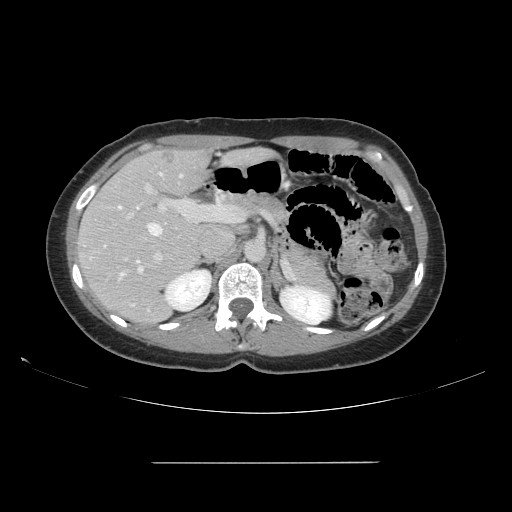
Contrast-enhanced abdominal CT, one axial slice. Position 95 of 151 along the scan axis. Soft-tissue window (W 400 / L 40 HU). 2.5 mm slice thickness. 512 × 512 image matrix. Female patient, age 46 years. Case-level facts recorded for this patient, not image findings: diagnosis: colorectal cancer liver metastases, imaged before liver resection; multiple liver metastases: yes; largest metastasis: 3 cm; disease in both lobes: yes.
Structures marked on this image (outlined manually by an expert reader):
- hepatic veins: bounding box <117,173,183,277> (left, top, right, bottom; pixels)
- liver: <79,150,209,323>
- planned liver remnant (the part of the liver to remain after resection): <90,151,210,263>
- portal vein (with intrahepatic branches): <125,183,238,263>
- liver metastasis: <162,151,179,165>